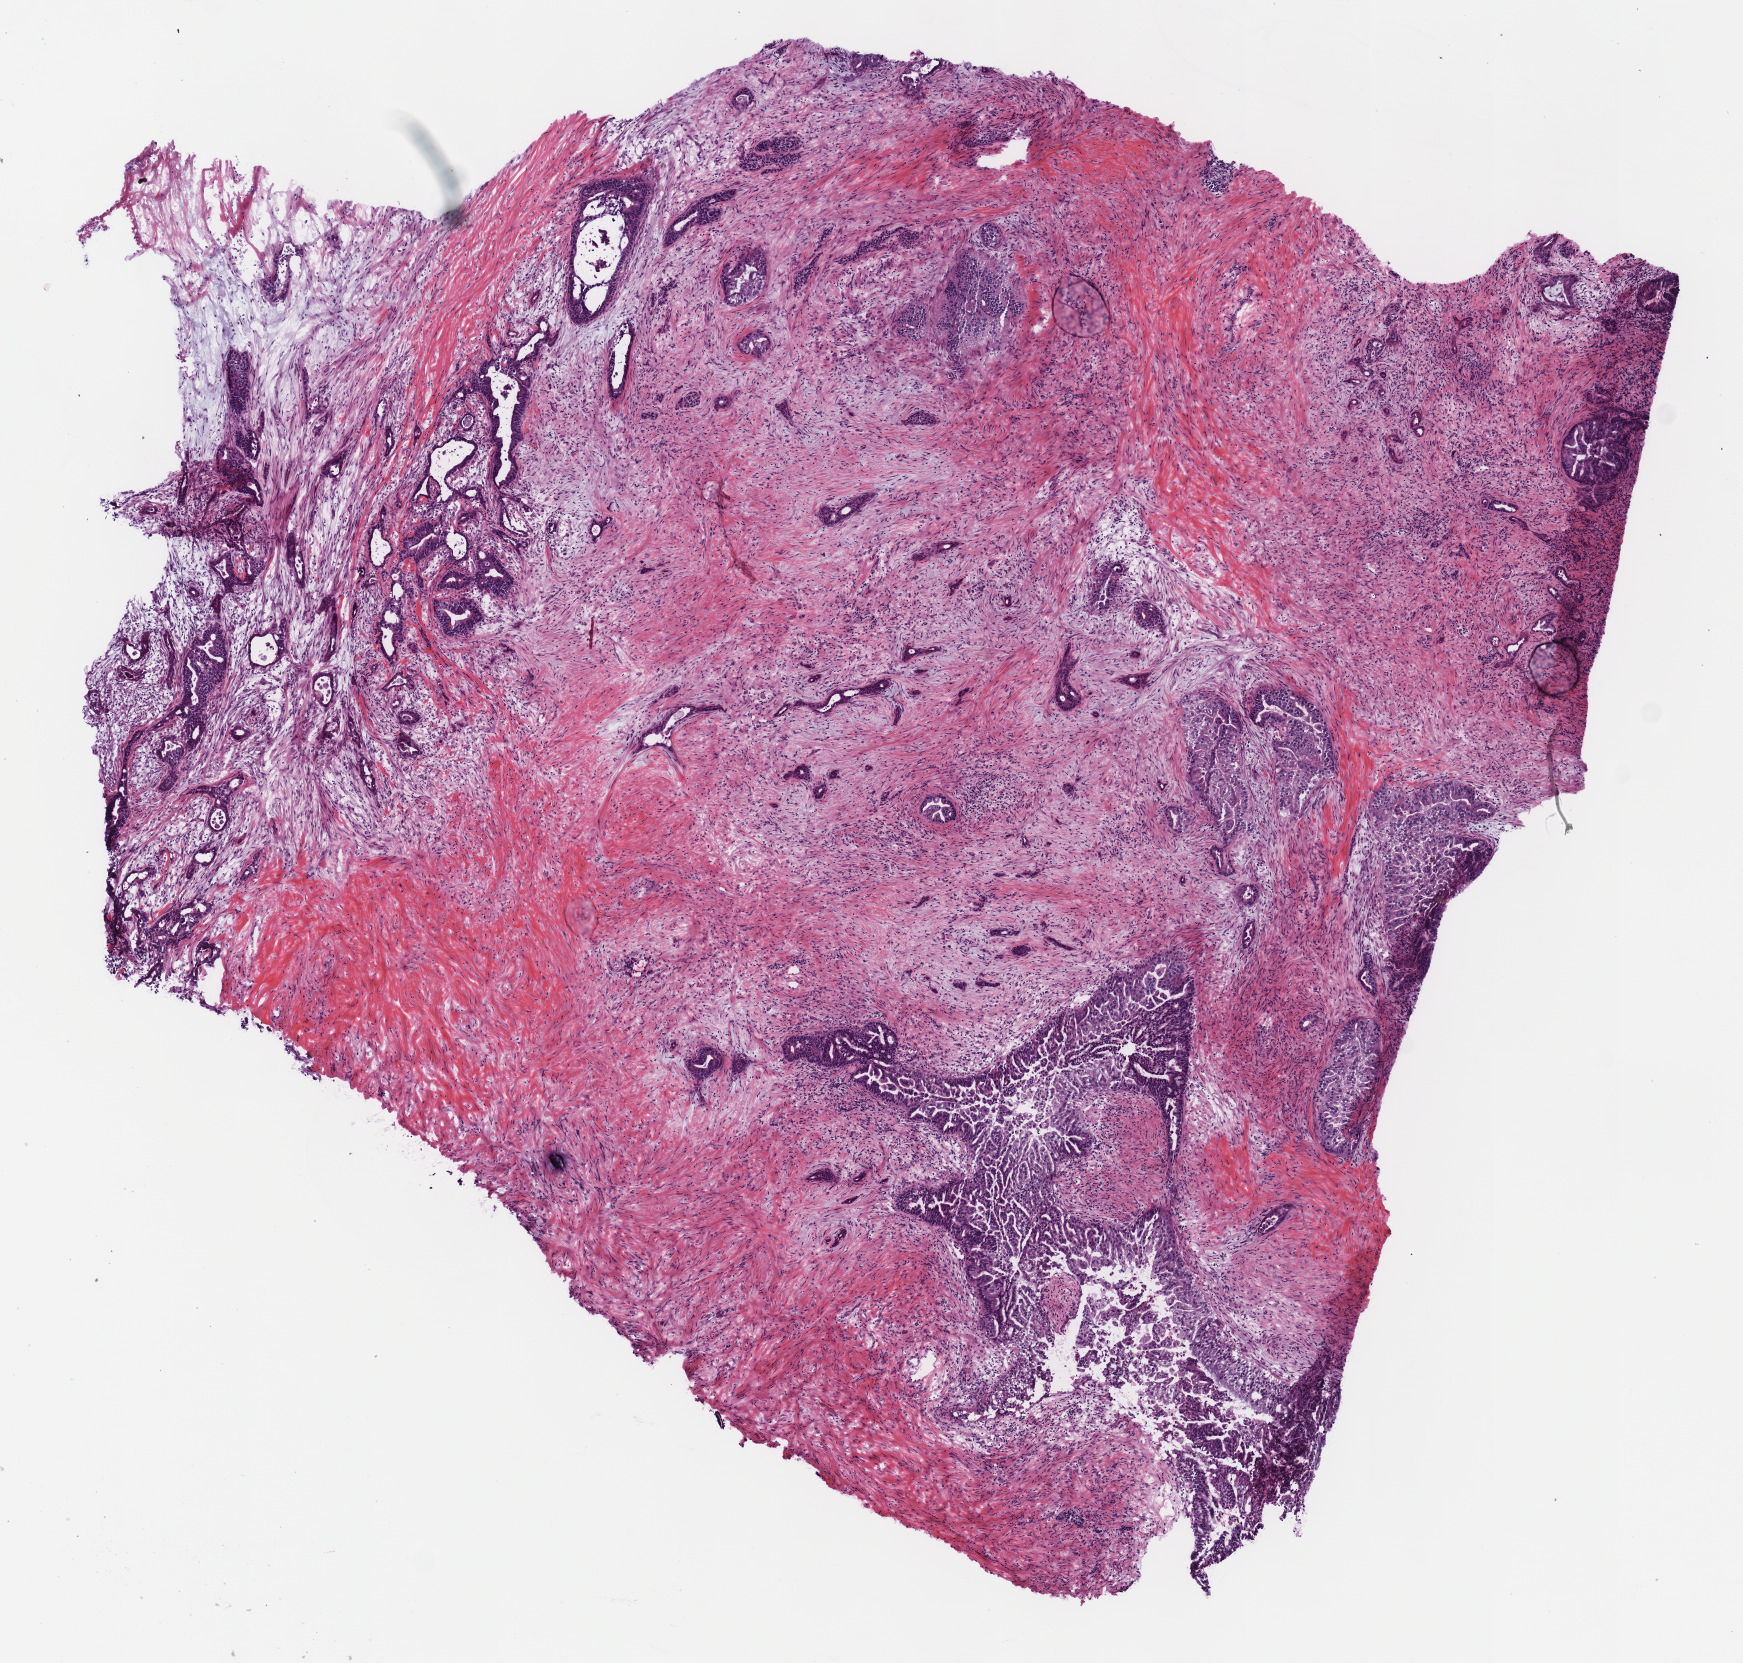
Whole-slide histology image, H&E — shown as a low-resolution overview of the whole scanned area (about 6.9 x 6.5 mm). Frozen section. Sample: primary tumour, pancreas. Patient: female, age at initial diagnosis 58 years. Histologic grade: G3 (poorly differentiated). Composition of this section per pathologist review: tumour cells 30%, tumour nuclei 25%, normal cells 0%, stromal cells 70%, necrosis 0%.
AJCC pathologic stage: IV (7th edition). Pathologic diagnosis: Infiltrating duct carcinoma, NOS (tail of pancreas).